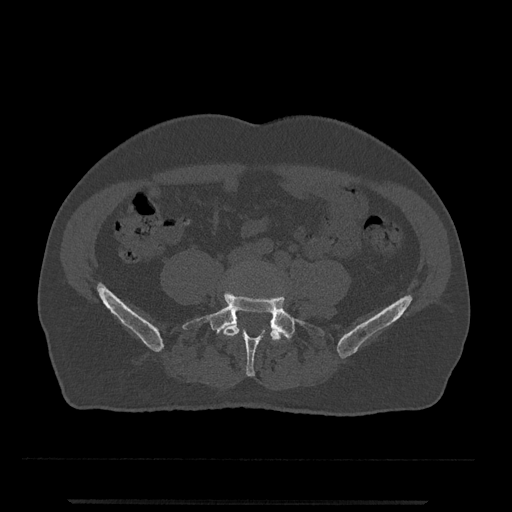
CT including the spine, one axial slice. Position 90 of 797 along the scan axis. Bone window (W 1800 / L 400 HU). 0.5 mm slice thickness. 512 × 512 image matrix, field of view 419 × 419 mm. Patient: male, 63 years. Case-level facts recorded for this patient, not image findings: primary cancer: prostate.
Structures marked on this image (semi-automatically segmented with operator editing):
- L4 vertebra: bounding box <222,319,283,342> (left, top, right, bottom; pixels)
- L5 vertebra: <183,292,324,377>